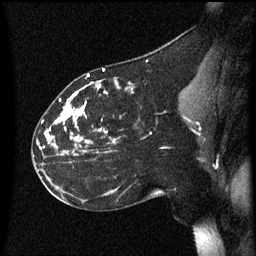
Breast MRI (dynamic contrast-enhanced), one sagittal slice. Slice 29 of 60 in the series (ordered by position). Dynamic contrast-enhanced series, image 2 of 3 at this slice position (ordered by acquisition). 1.5 T. TE 4.2 ms, TR 8.4 ms. 256 × 256 image matrix, field of view 200 × 200 mm. Patient: female, 35 years. From the clinical record (not read from this slice): setting: breast cancer imaged before/during neoadjuvant chemotherapy; receptor status: HER2-positive.
Annotated regions visible in this slice (semi-automatically segmented with operator editing):
- analysis volume of interest (the breast-tissue region the enhancement analysis was run in; not a lesion): bounding box [x1, y1, x2, y2] px = [32, 72, 160, 173]
- tumour enhancement mask (voxels above the 70 % enhancement threshold inside the analysis volume of interest): [40, 74, 118, 157]